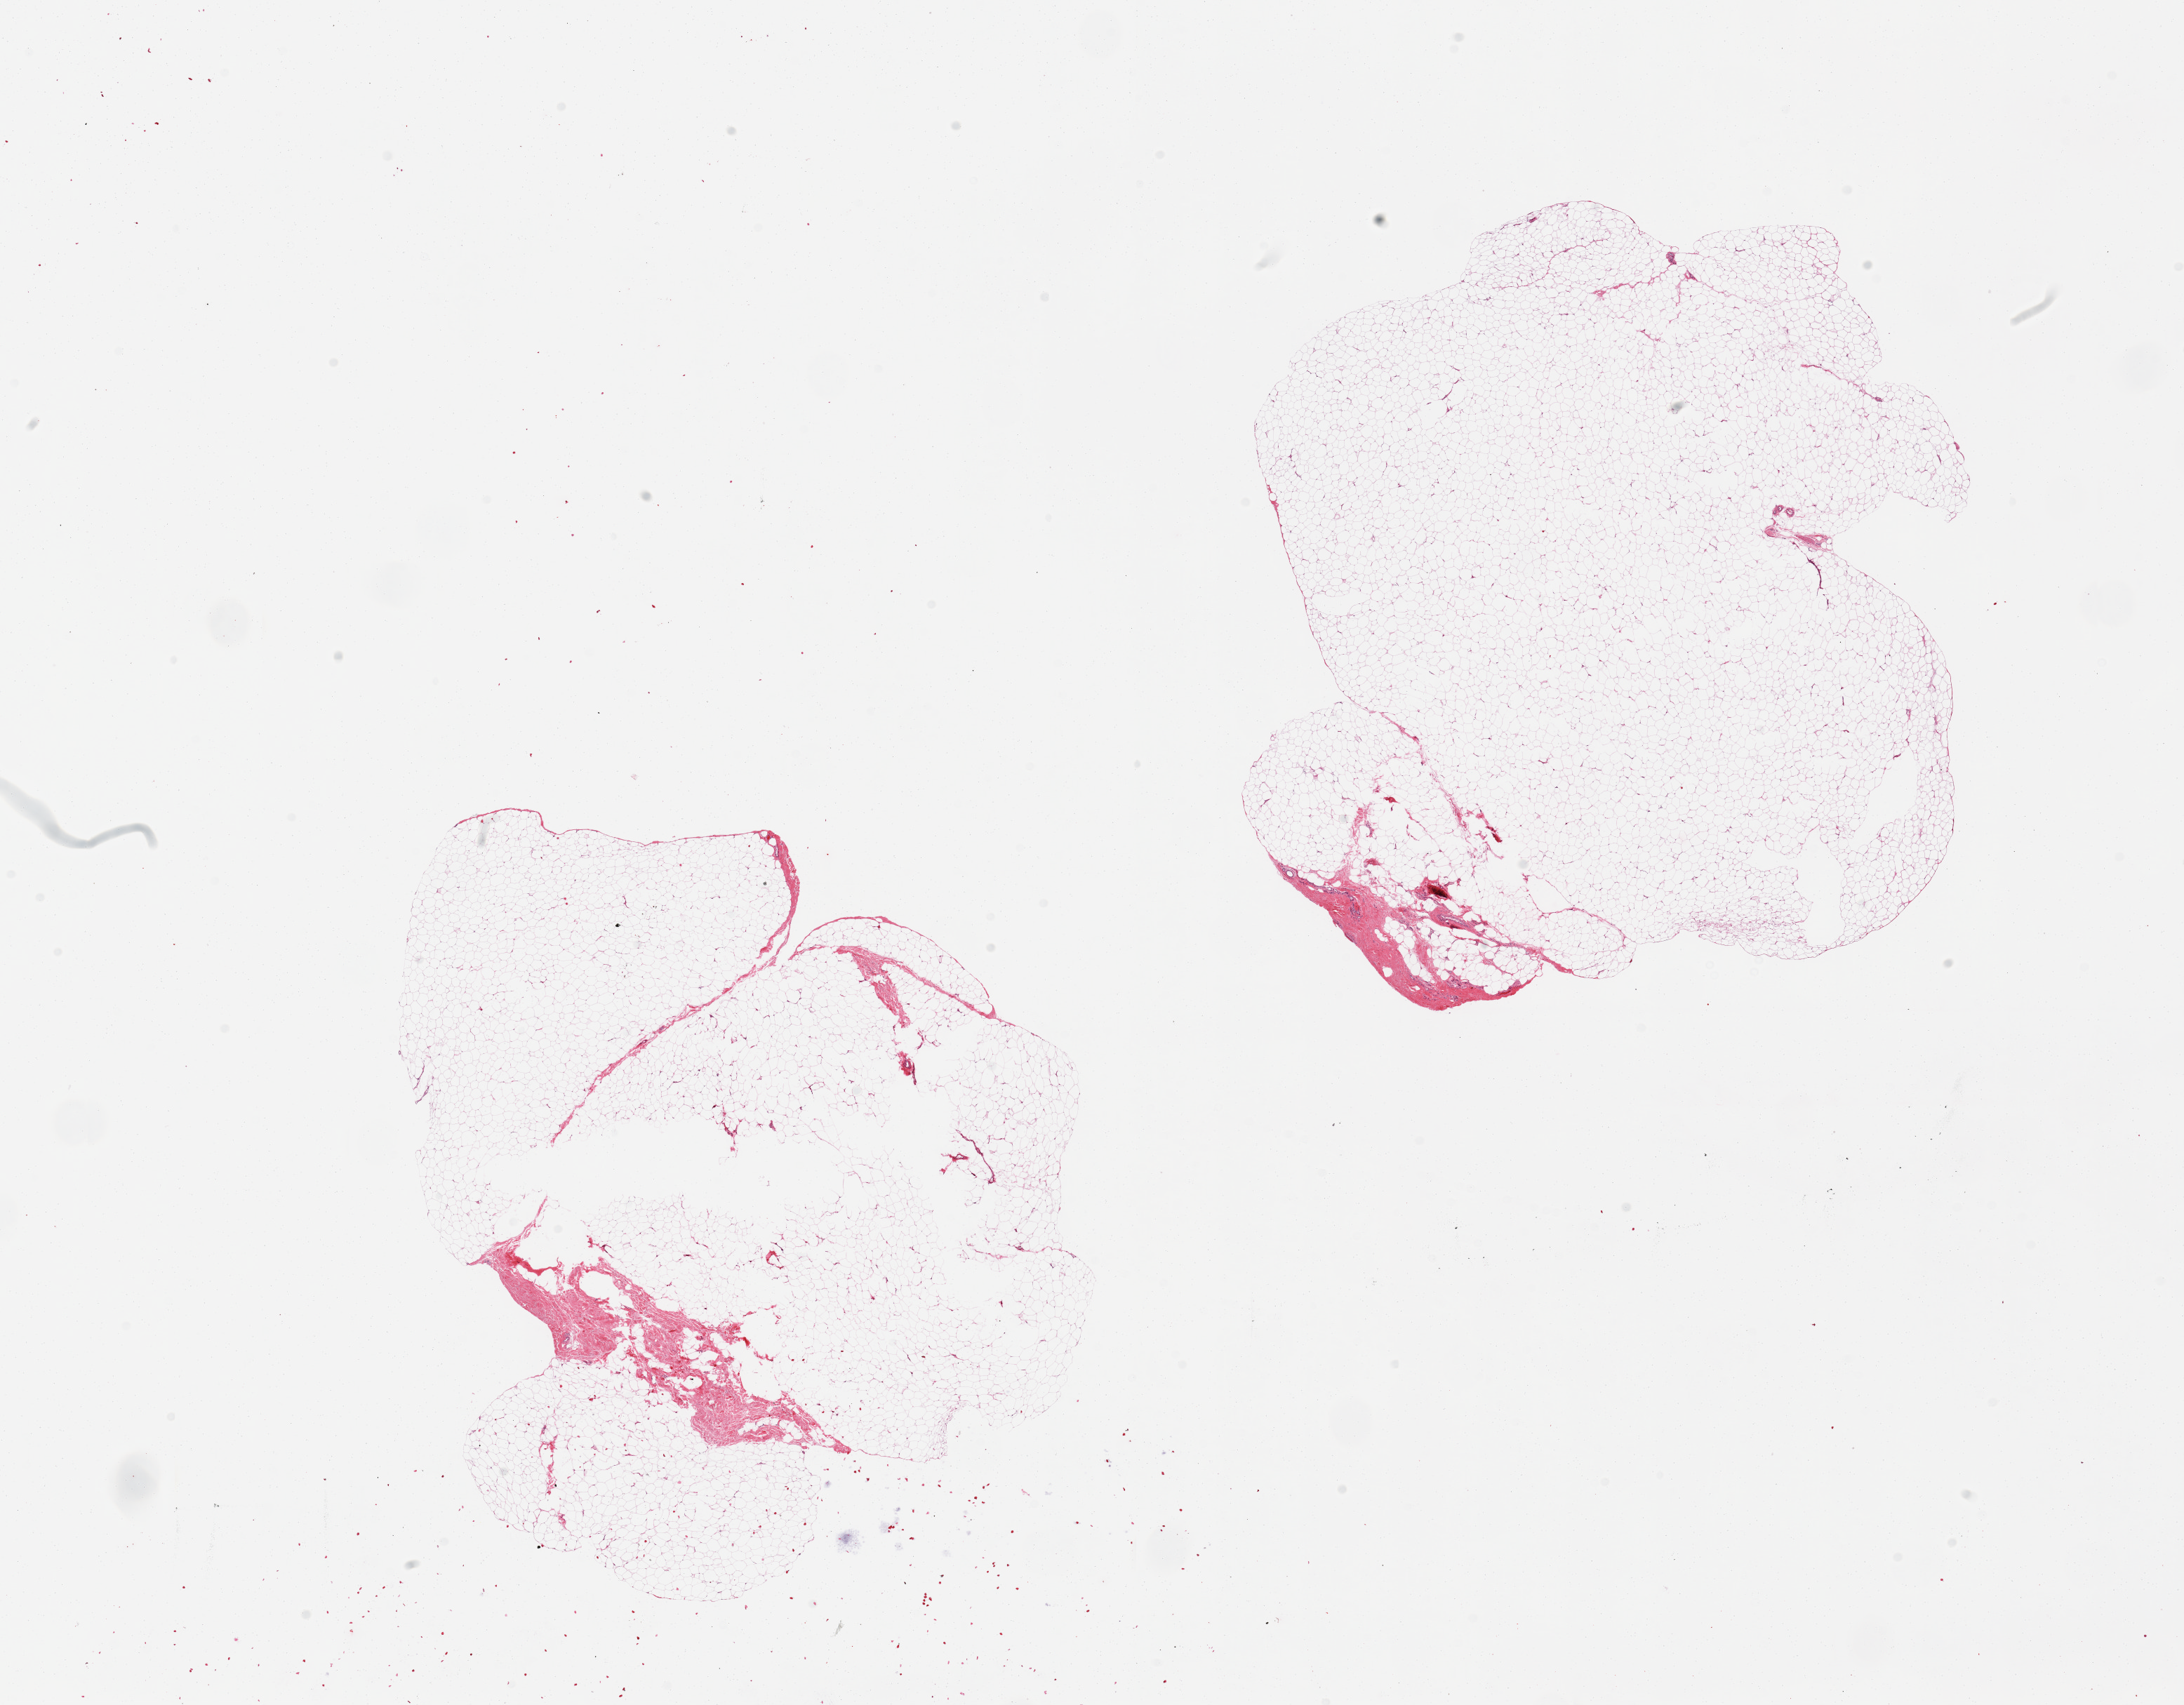
H&E whole-slide image — whole scanned area (about 24.6 x 19.2 mm) shown as a low-resolution overview. PAXgene-fixed paraffin-embedded (PFPE) section. Target tissue: breast. Donor tissue sample. Donor sex: male.
- review note (as recorded): 2 pieces, ~5-10% fascia/fibrous tissue, rest adipose tissue; No ductal elements